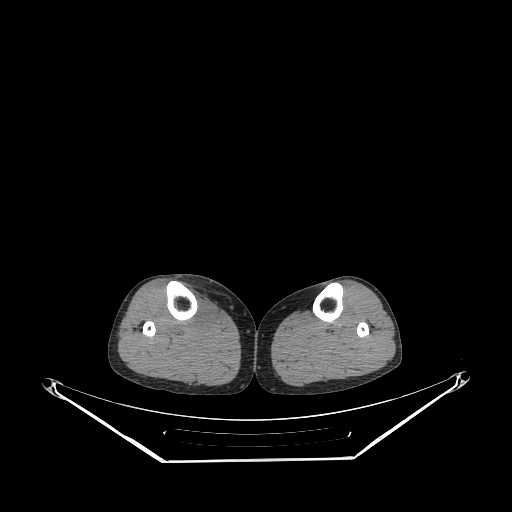
CT of an extremity soft-tissue mass (from a PET/CT study), one axial slice; position 146 of 267 along the scan axis; reconstruction kernel STANDARD; 140 kVp; soft-tissue window (W 400 / L 40 HU); 3.75 mm slice thickness; 512 × 512 image matrix. Female patient. Case-level facts recorded for this patient, not image findings: histological type: undifferentiated – high grade; grade: high; site of the primary tumour: right thigh.
Outlined on this slice (expert contour drawn on MRI and transferred to this co-registered scan by the dataset authors):
- gross tumour volume (mass): bounding box <185,292,215,330> (left, top, right, bottom; pixels)